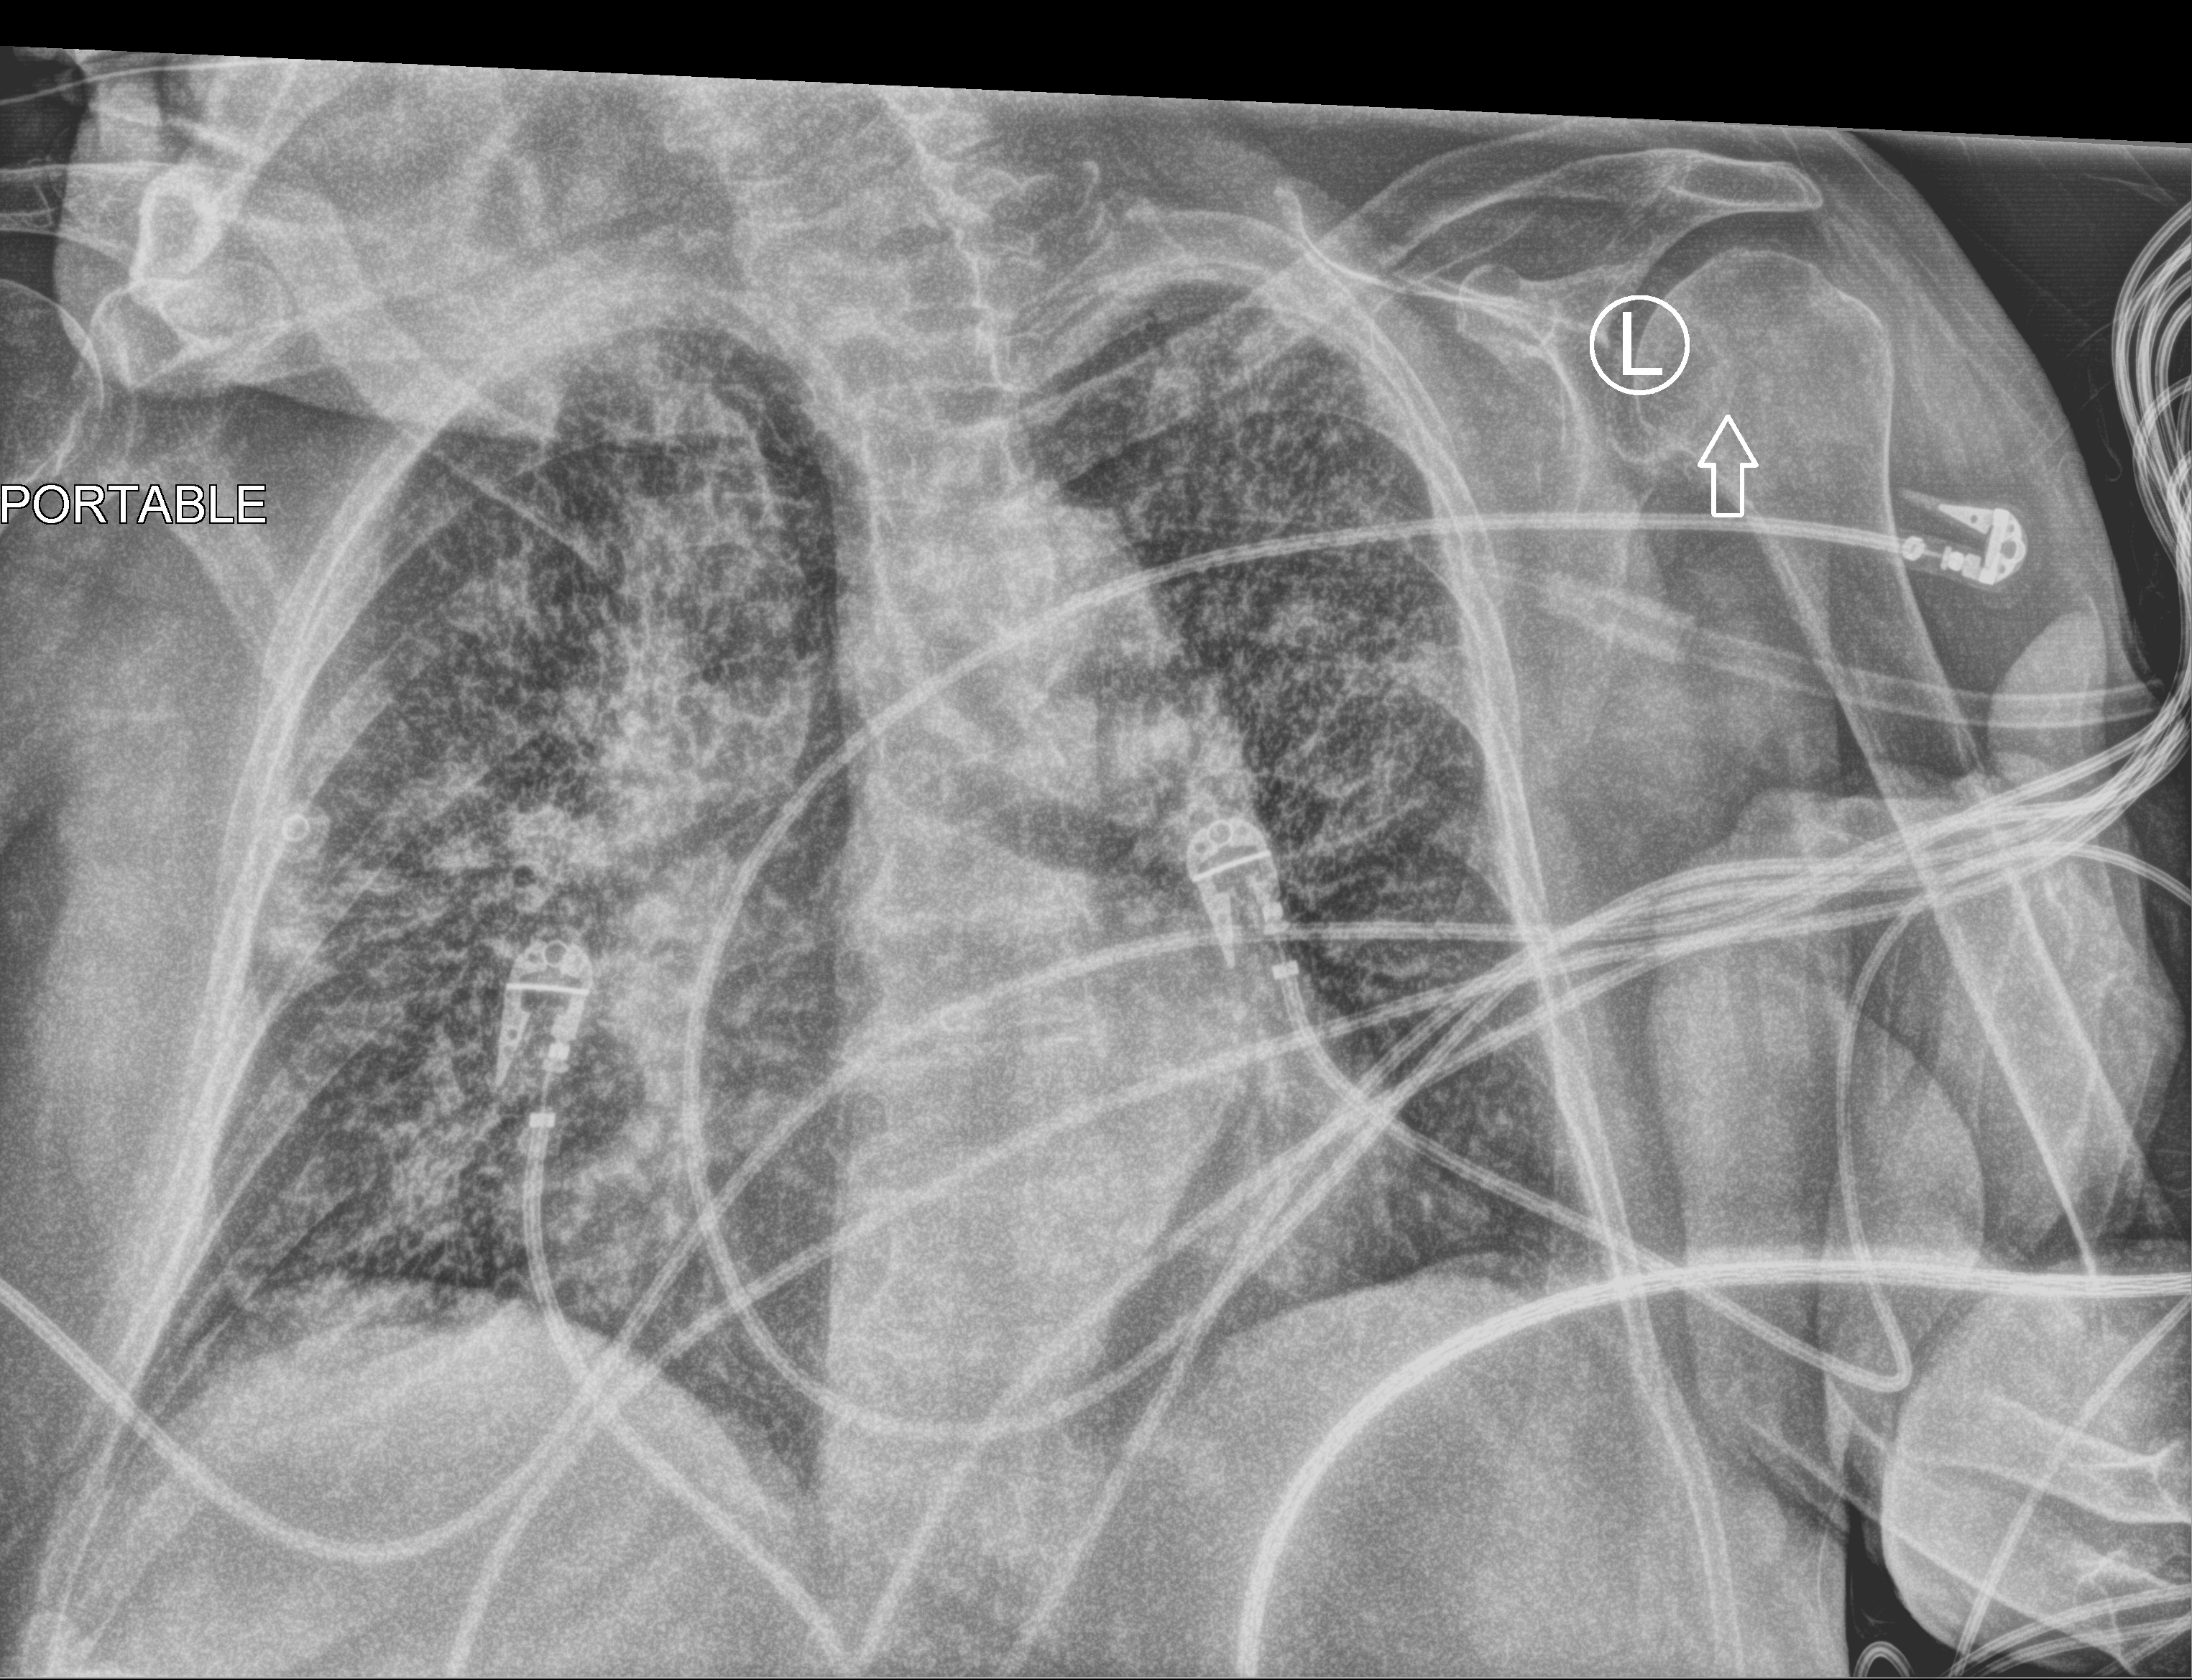
Bedside chest radiograph (computed radiography); anteroposterior (AP) projection. Patient hospitalised with COVID-19; female, aged 75–90 years.
From the hospital-stay record, not from the radiograph (when in the stay this image was taken is not recorded): hypertension (admission record): yes.